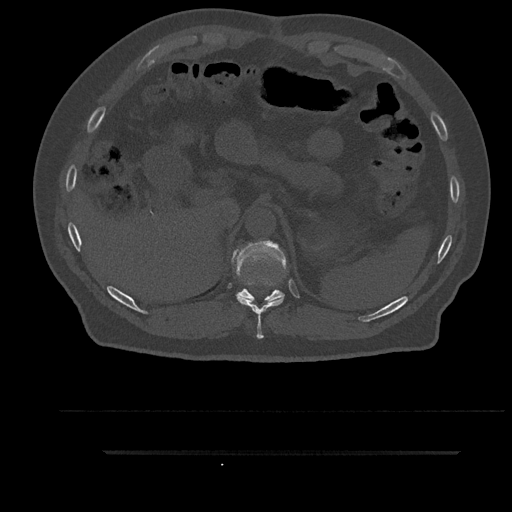
CT including the spine, one axial slice; position 335 of 797 along the scan axis; reconstruction kernel Br40s/3; 120 kVp; bone window (W 1800 / L 400 HU); 0.5 mm slice thickness; 512 × 512 image matrix, field of view 432 × 432 mm. Patient: male, 63 years. Case-level facts recorded for this patient, not image findings: primary cancer: renal; vertebrae with lytic lesions (as recorded): T8.
Annotated regions visible in this slice (semi-automatic segmentation, software-assisted and operator-edited):
- T10 vertebra: box from (x=236, y=296) to (x=284, y=339) px
- T11 vertebra: (x=233, y=240)–(x=286, y=304)